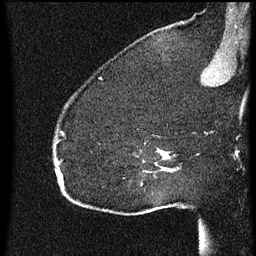
Breast MRI (dynamic contrast-enhanced), one sagittal slice. Position 49 of 60 along the scan axis. Dynamic contrast-enhanced series, image 2 of 3 at this slice position (ordered by acquisition). 1.5 T. TE 4.2 ms, TR 8 ms. 2 mm slice thickness. 256 × 256 image matrix, field of view 180 × 180 mm. Patient: female, 52 years.
Annotated regions visible in this slice (semi-automatic segmentation, software-assisted and operator-edited):
- analysis volume of interest (the breast-tissue region the enhancement analysis was run in; not a lesion): bounding box (x1, y1, x2, y2) in pixels: (54, 126, 177, 207)
- tumour enhancement mask (voxels above the 70 % enhancement threshold inside the analysis volume of interest): (56, 132, 170, 175)